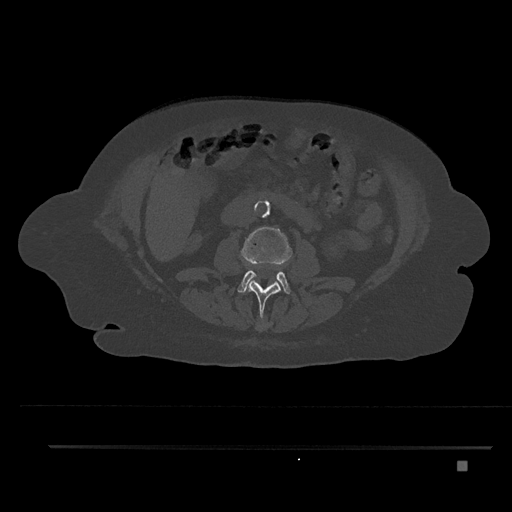
CT including the spine, one axial slice; slice 154 of 797 in the series (ordered by position); 120 kVp; bone window (W 1800 / L 400 HU); 512 × 512 image matrix, field of view 437 × 437 mm. Female patient, age 76 years. From the clinical record (not read from this slice): primary cancer: lung; vertebrae with lytic lesions (as recorded): T11, L3.
Annotated regions visible in this slice (semi-automatically segmented with operator editing):
- L1 vertebra: bounding box [x1, y1, x2, y2] px = [256, 325, 263, 329]
- L2 vertebra: [246, 280, 281, 329]
- L3 vertebra: [238, 227, 293, 294]